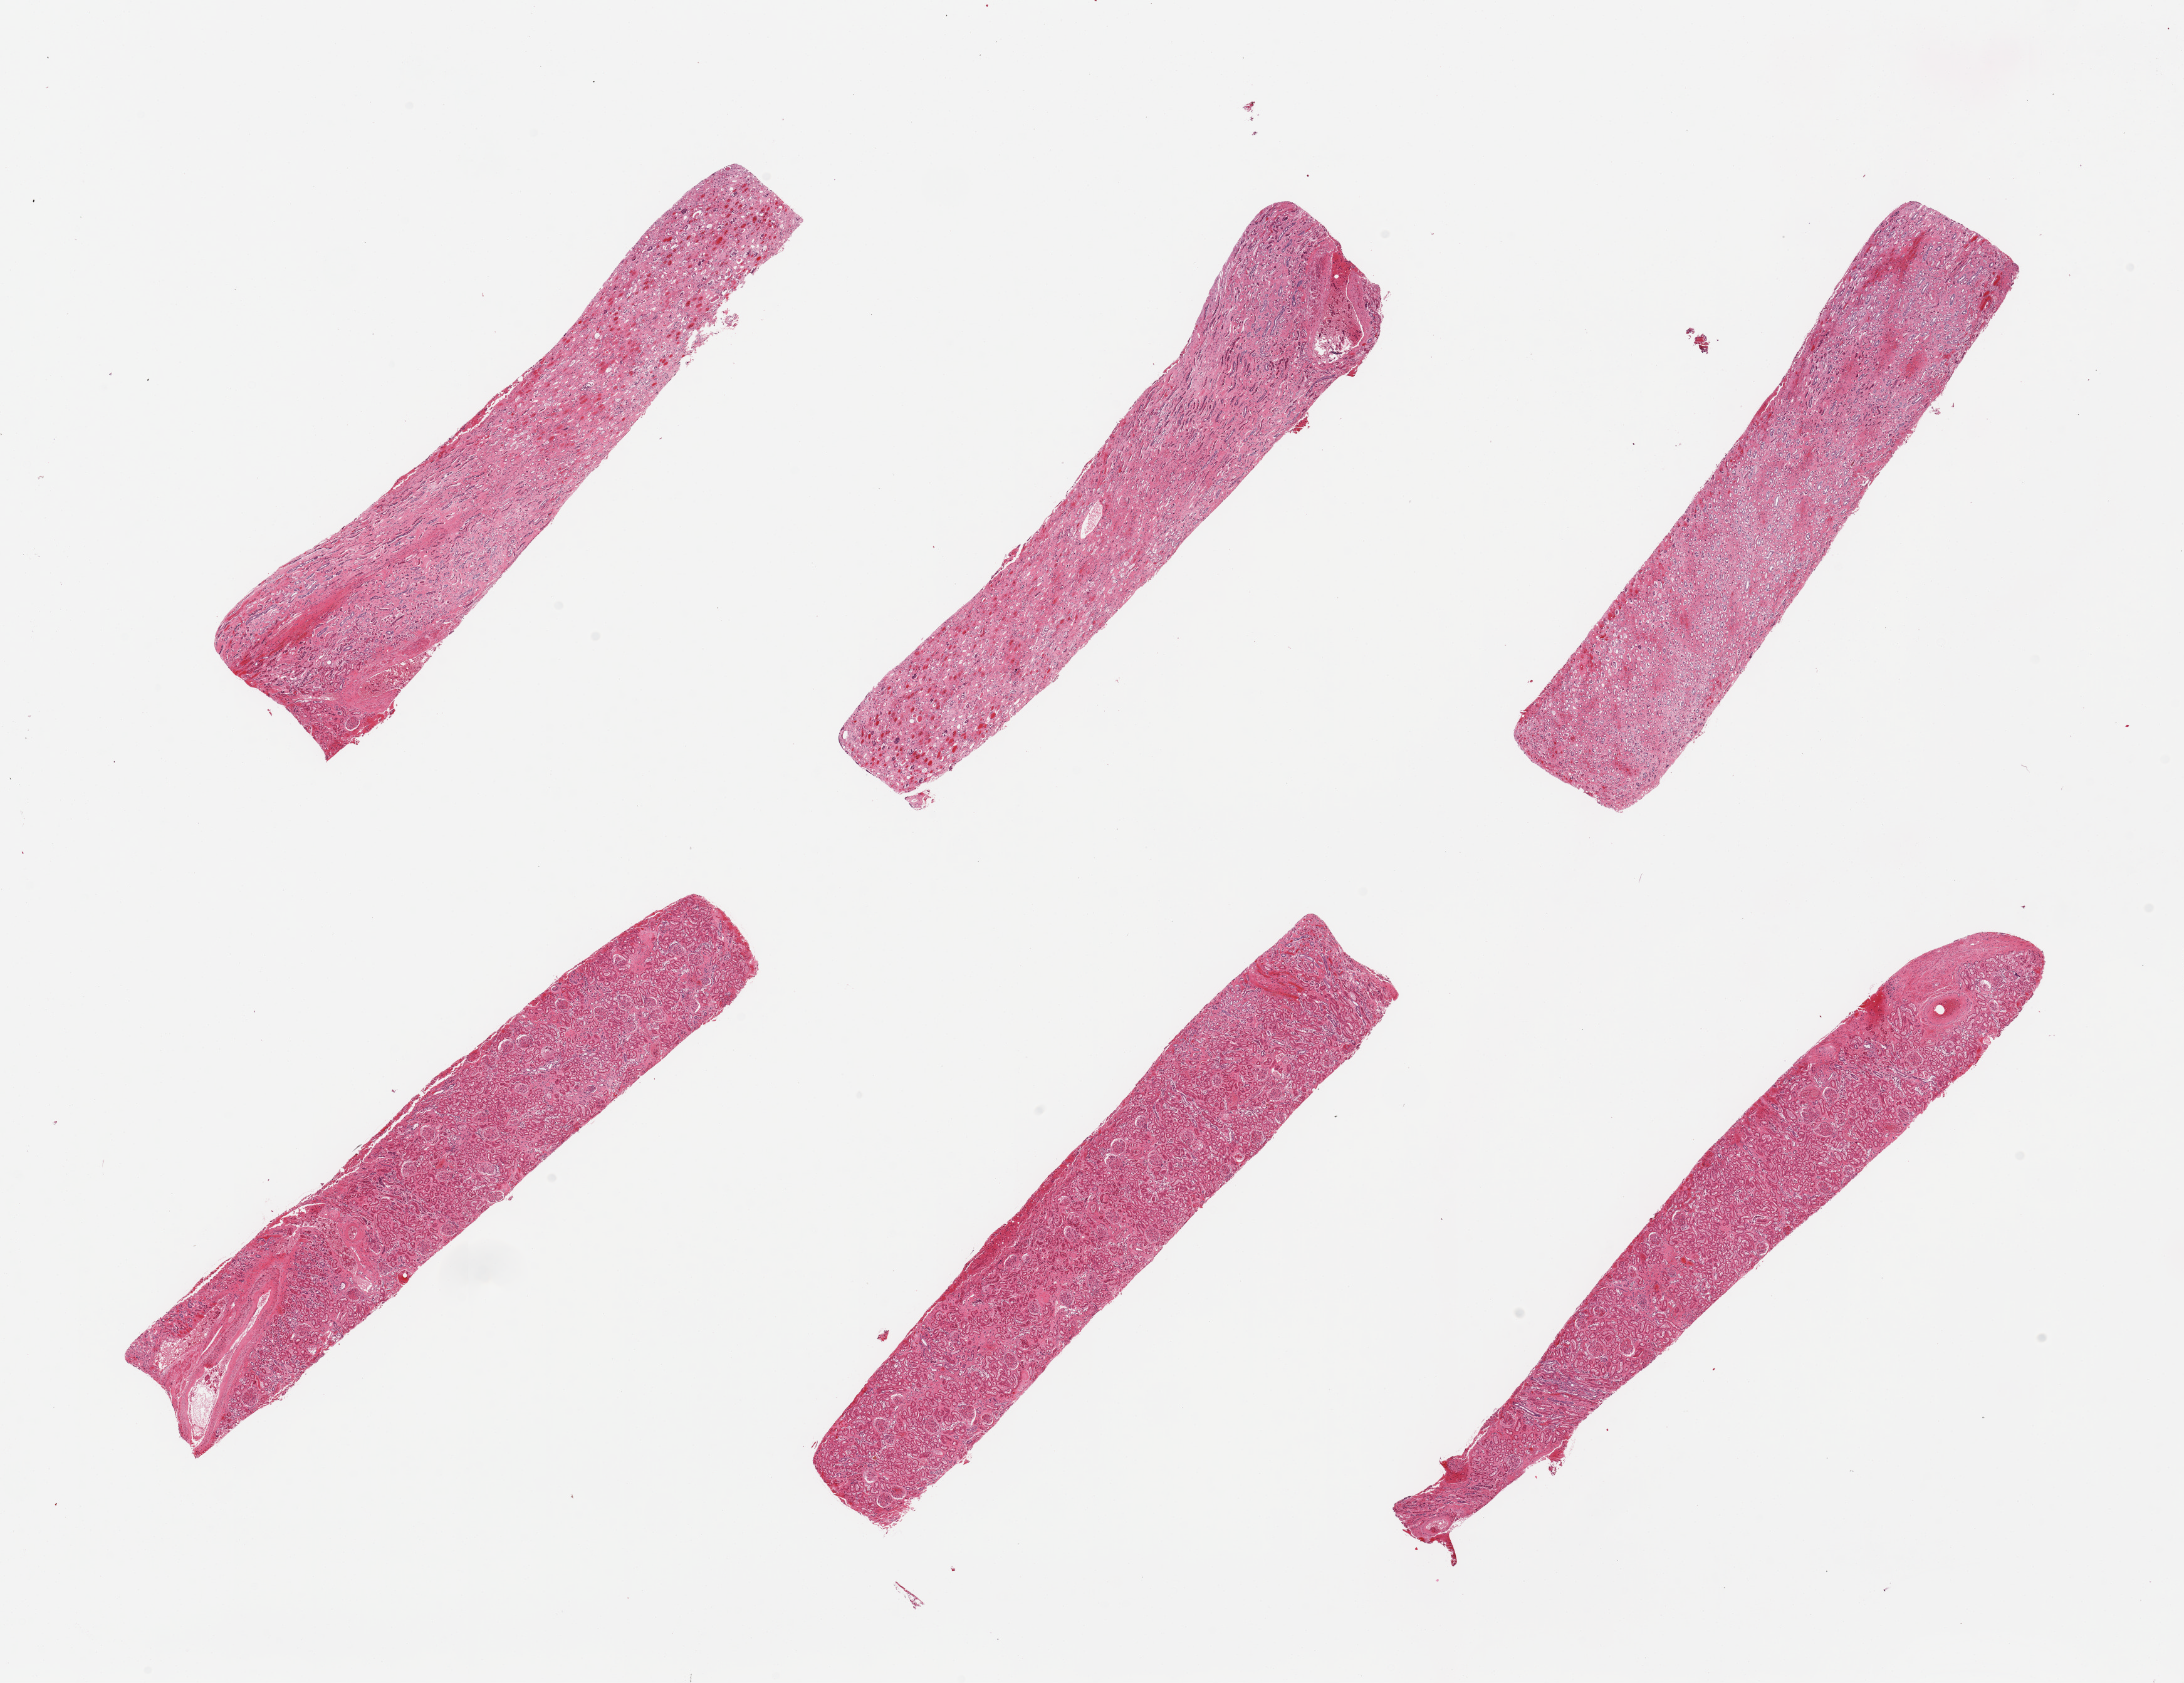
H&E whole-slide image — a low-resolution overview of the entire scanned area, about 27.6 x 21.2 mm (acquisition: 20x scan). PAXgene-fixed paraffin-embedded (PFPE) section. Target tissue: renal cortex. Donor tissue sample. Donor: male.
Pathologist's review note for this sample: 6 pieces; cortex and medulla (not target), few sclerotic glomeruli seen, arteriosclerosis.